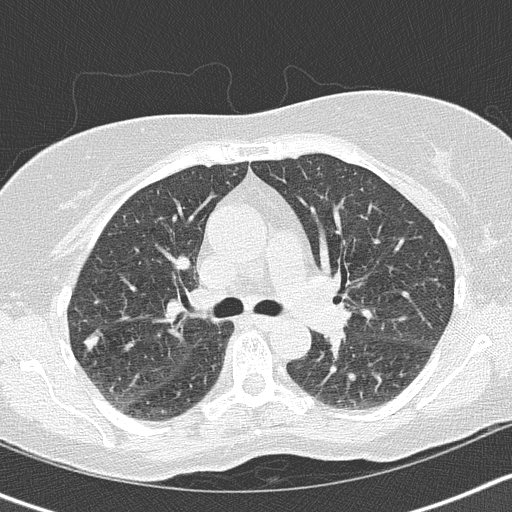
Low-dose screening chest CT, axial slice. Baseline annual screen. Lung window (W 1500 / L -600 HU). Lung (sharp) reconstruction kernel (B50f). 120 kVp. Female, age 61 years at enrolment. Current smoker at enrolment.
Expert reader's lesion annotation, box from (x=67, y=320) to (x=117, y=365) px. No non-calcified nodule or mass ≥4 mm was recorded by the screening reader at this exam. Participant outcome: lung cancer diagnosed 486 days after this screen — small cell carcinoma, NOS, right upper lobe, stage IIIA (AJCC 6th edition), 7 mm at pathology.